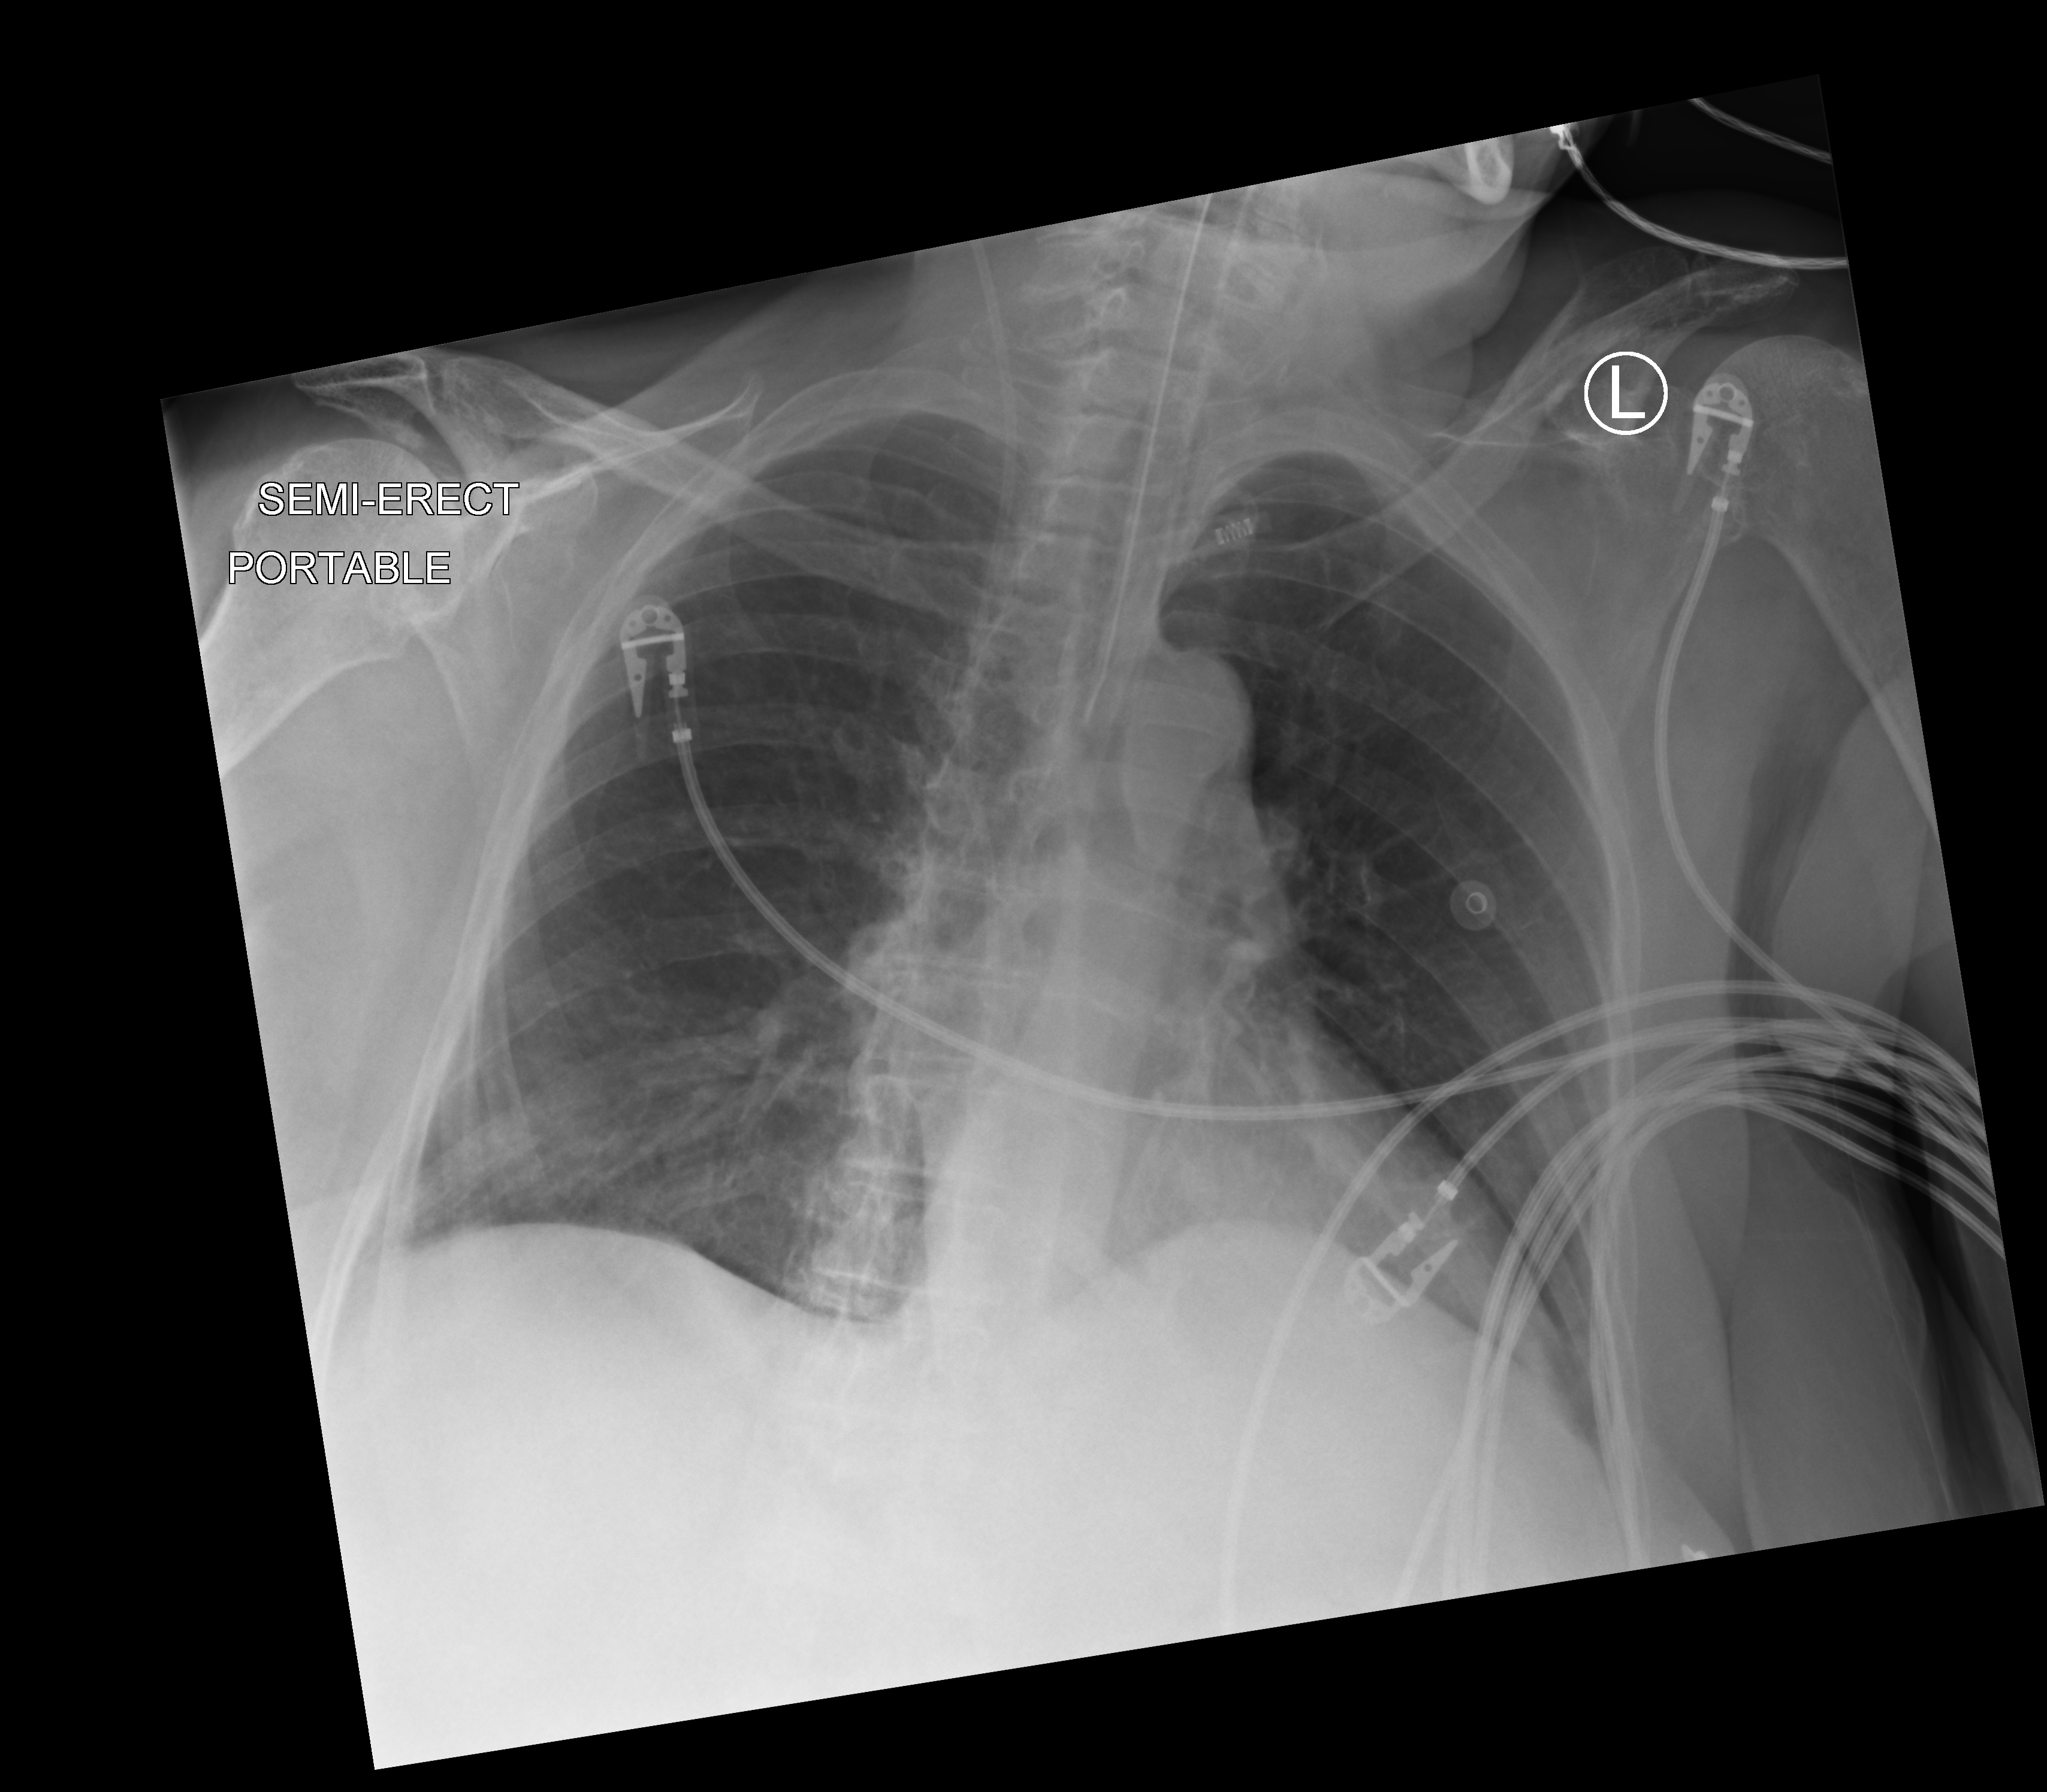
Chest X-ray (portable), anteroposterior (AP) projection. Female patient hospitalised with COVID-19, age 75–90 years.
Hospital-stay facts (about this admission, not read from this image; timing relative to this image not recorded): admitted to intensive care during this hospital stay: yes.